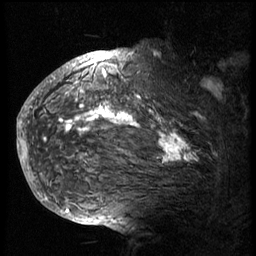
Breast MRI (dynamic contrast-enhanced), one sagittal slice; slice 53 of 74 in the series (ordered by position); 3 images stored at this slice position (order not interpretable as contrast timing); 1.5 T; TE 4.2 ms, TR 8.9 ms; 2.5 mm slice thickness; 256 × 256 image matrix. Female patient, age 57 years. From the clinical record (not read from this slice): setting: breast cancer imaged before/during neoadjuvant chemotherapy; receptor status: HER2-positive.
Outlined on this slice (semi-automatically segmented with operator editing):
- analysis volume of interest (the breast-tissue region the enhancement analysis was run in; not a lesion): box from (x=40, y=62) to (x=241, y=175) px
- tumour enhancement mask (voxels above the 140 % enhancement threshold inside the analysis volume of interest): (x=50, y=62)–(x=197, y=163)